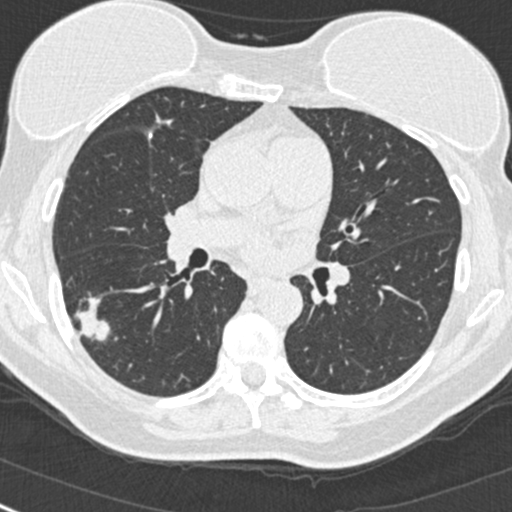
Low-dose screening chest CT, one axial slice. Slice 144 of 268 in the series (ordered by position). 120 kVp. Lung window (W 1500 / L -600 HU). 1 mm slice thickness. 512 × 512 image matrix, field of view 296 × 296 mm.
Annotated regions visible in this slice (expert manual segmentation):
- lesion 1 (tumor, upper lobe of right lung): bounding box (x1, y1, x2, y2) in pixels: (76, 297, 110, 341)